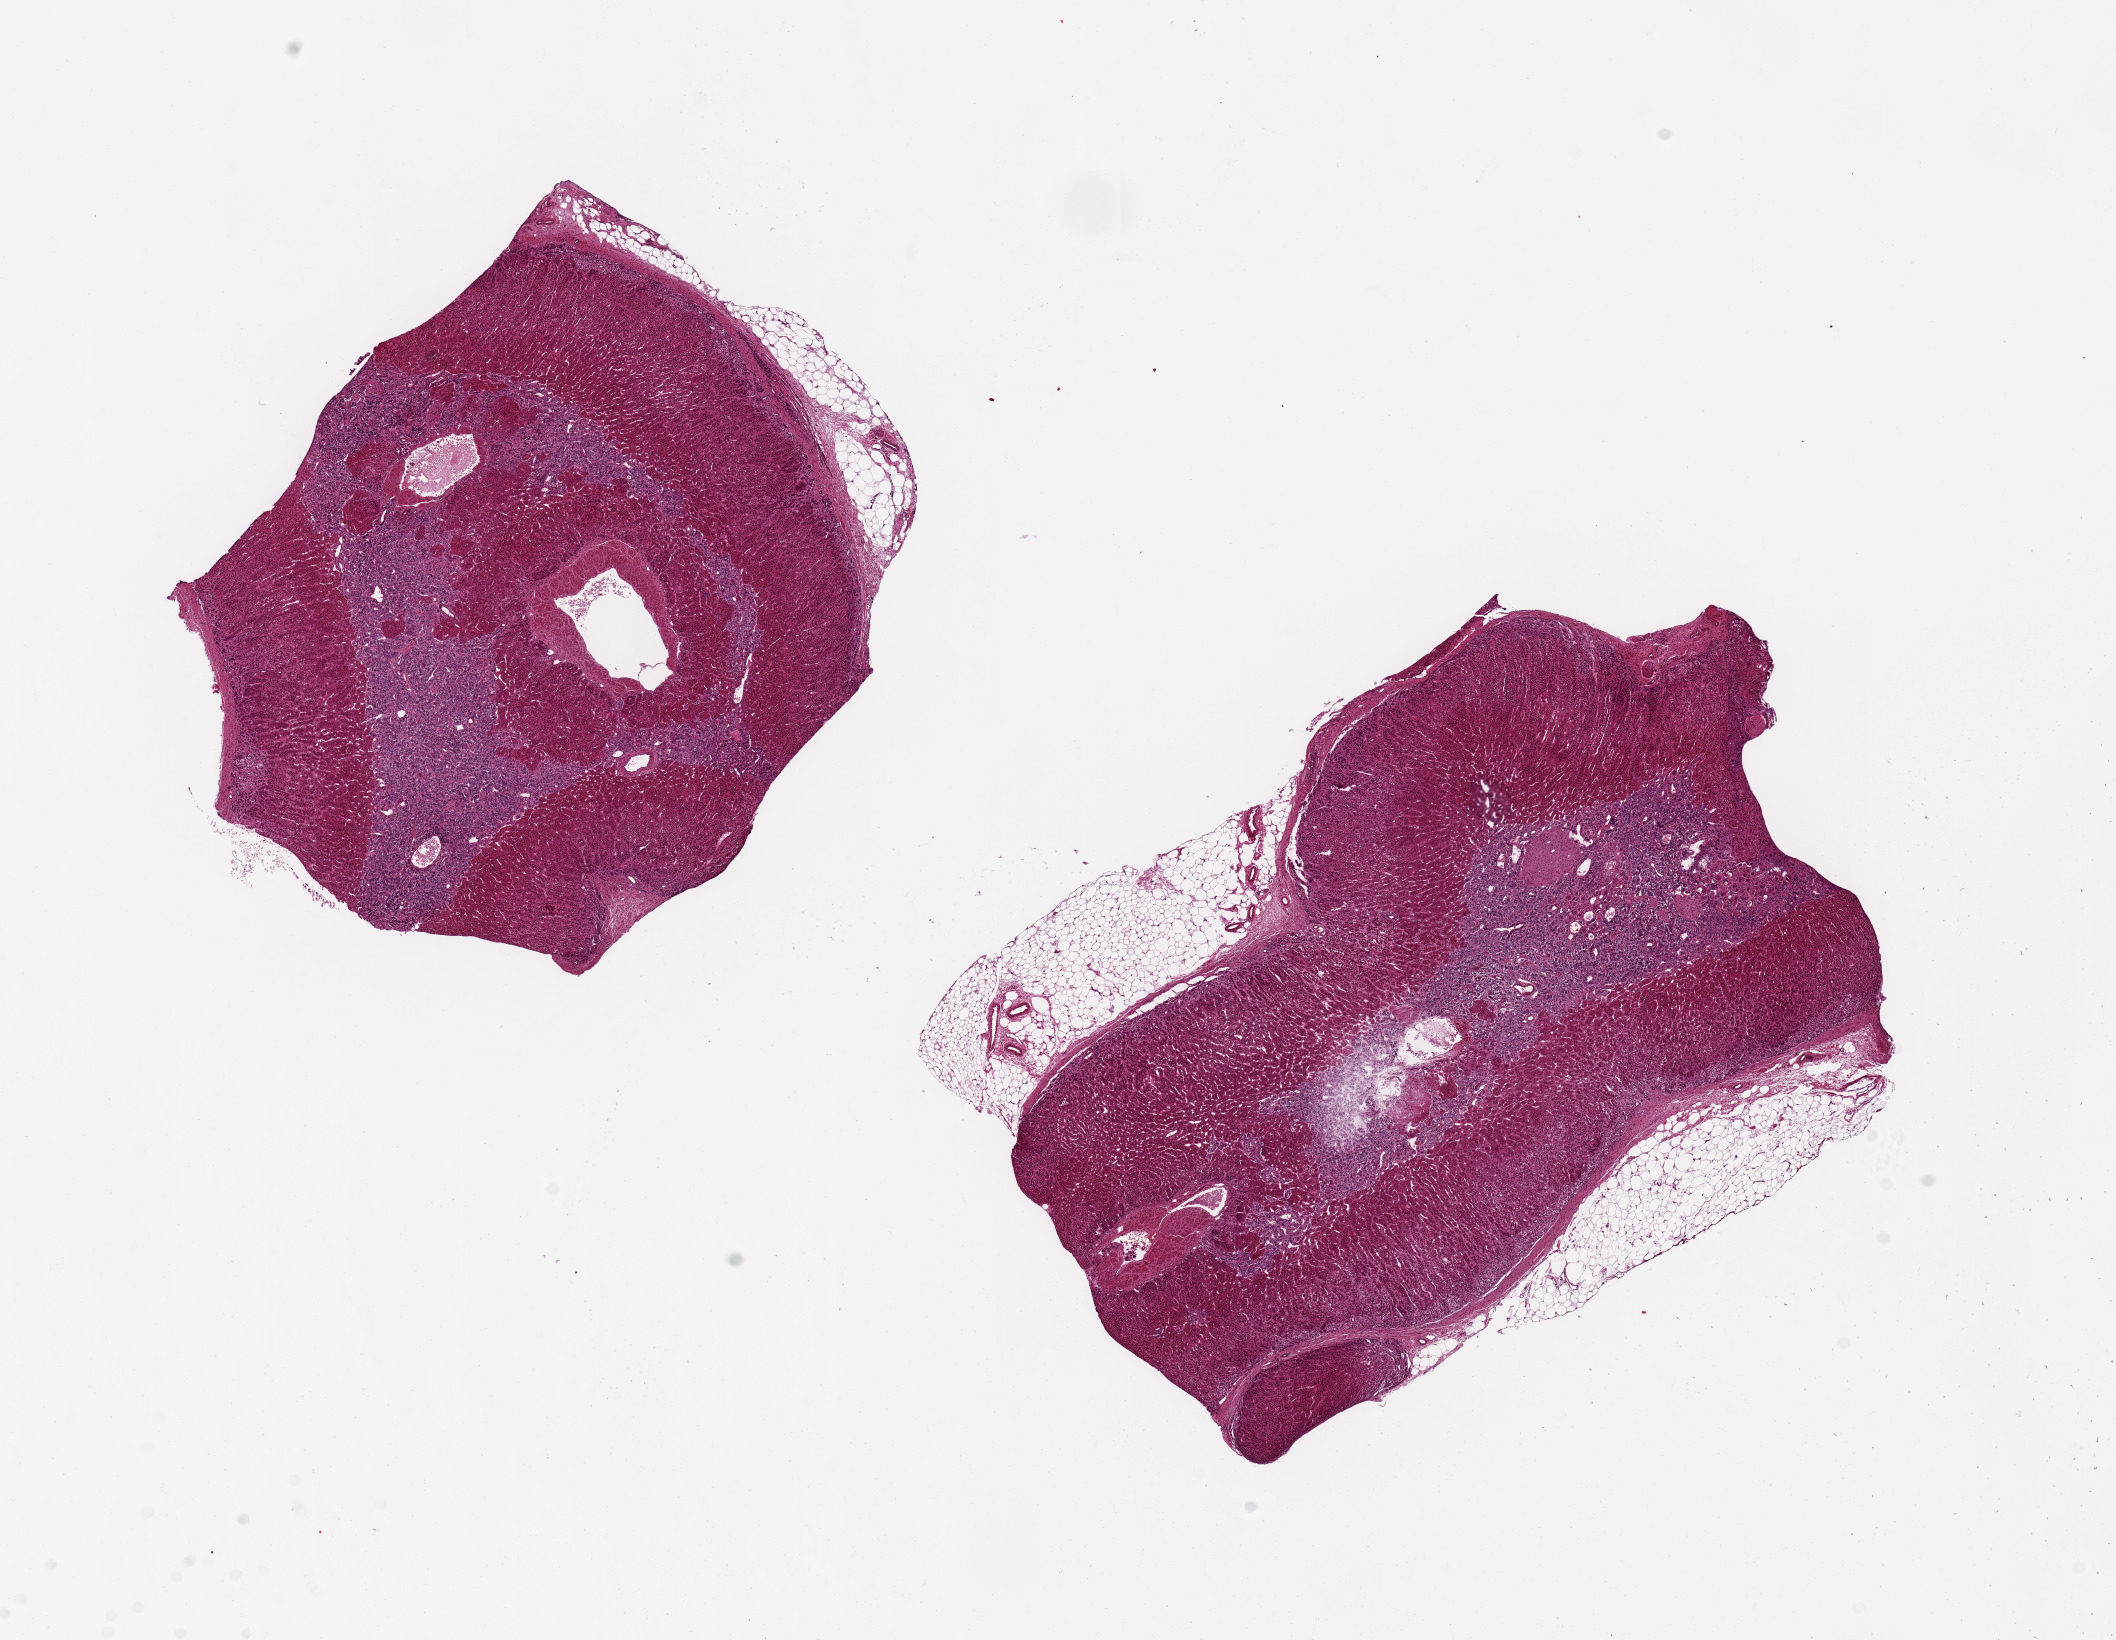
Whole-slide image, hematoxylin and eosin (H&E) stain — whole scanned area (about 16.7 x 13.0 mm) shown as a low-resolution overview. PAXgene-fixed paraffin-embedded (PFPE) section. Section of adrenal gland (target tissue). Tissue donor sample. Donor: male.
* reviewer comment on this tissue sample: 2 ~6.5x4.5mm aliquots; both with partially autolyzed medulla and well-preserved cortex